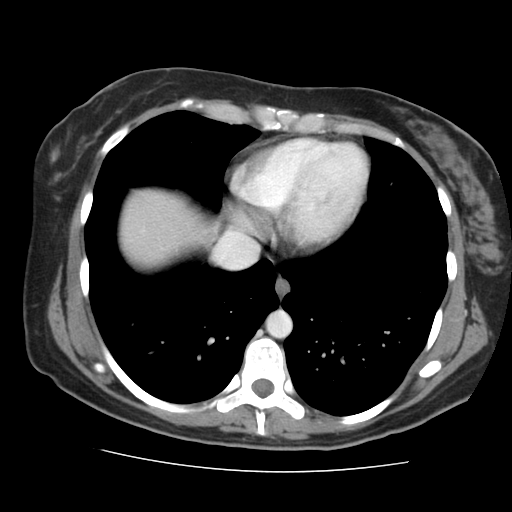
Contrast-enhanced abdominal CT, one axial slice; soft-tissue window (W 400 / L 40 HU); 512 × 512 image matrix, field of view 333 × 333 mm. Female patient, age 46 years. Case-level facts recorded for this patient, not image findings: diagnosis: colorectal cancer liver metastases, imaged before liver resection; multiple liver metastases: no; largest metastasis: 2.8 cm; disease in both lobes: no.
Outlined on this slice (outlined manually by an expert reader):
- hepatic veins: bounding box (x1, y1, x2, y2) in pixels: (216, 238, 257, 268)
- liver: (122, 190, 210, 266)
- planned liver remnant (the part of the liver to remain after resection): (122, 190, 210, 266)